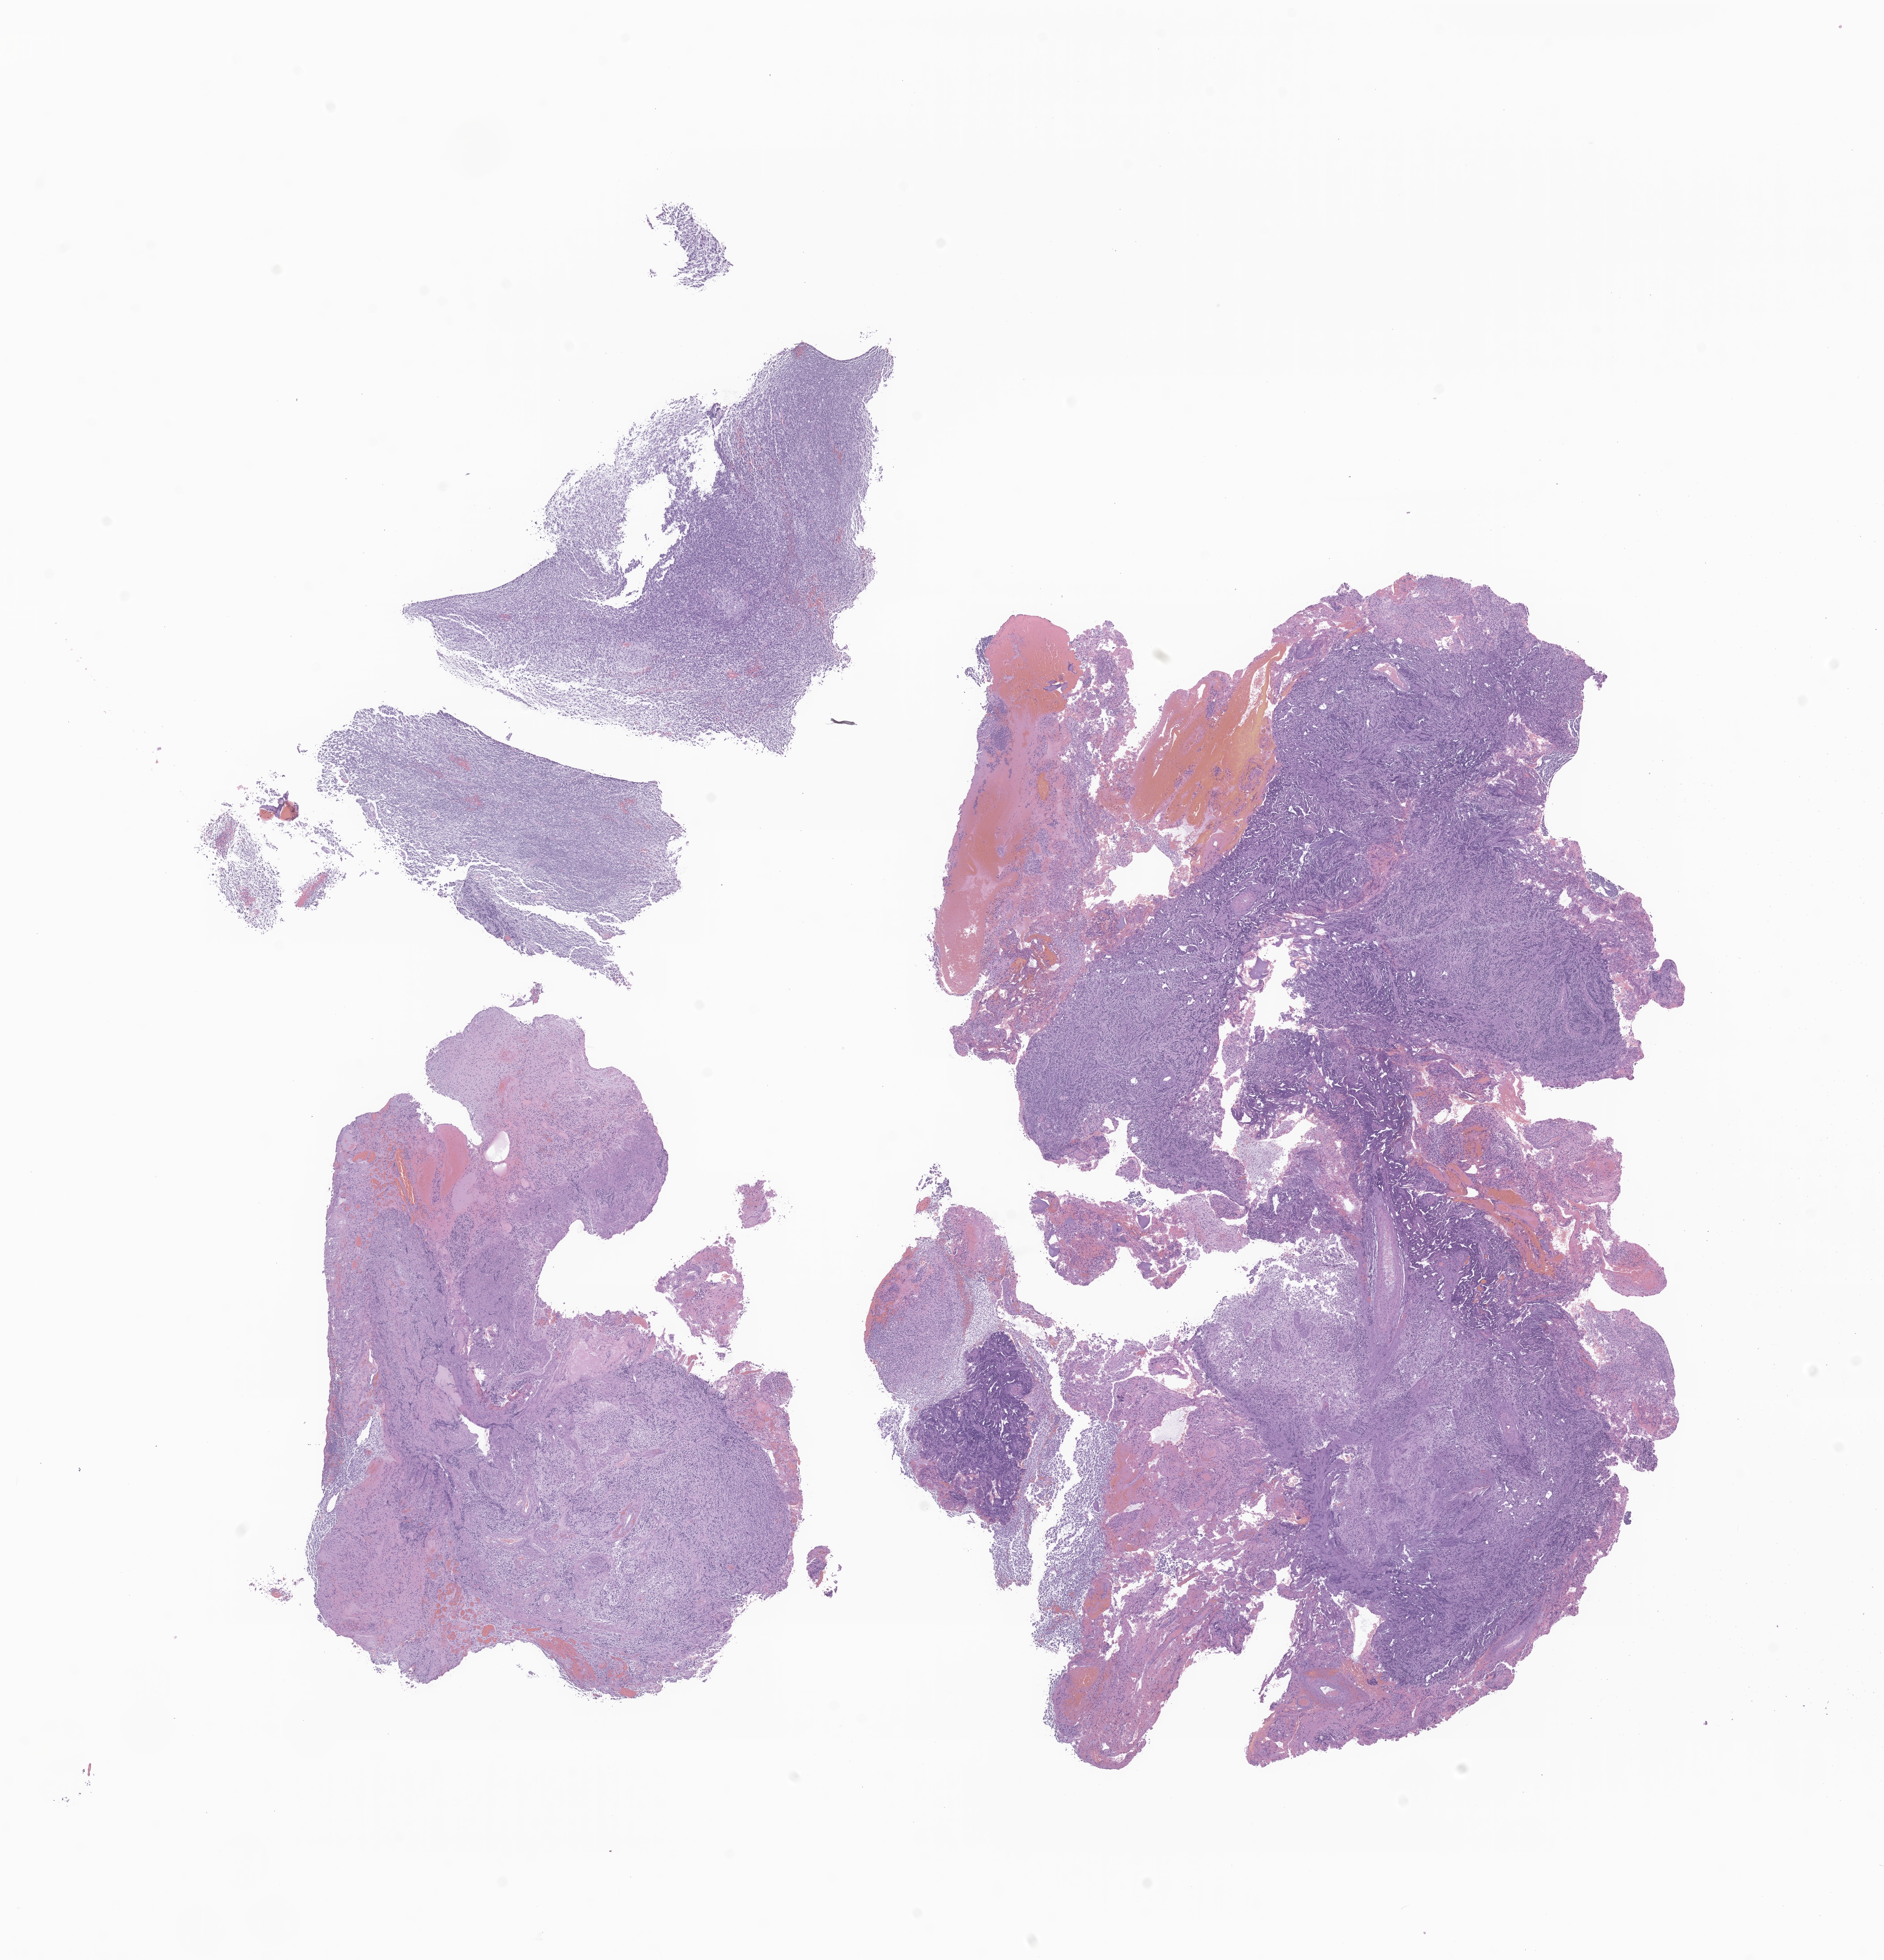
Hematoxylin and eosin (H&E) whole-slide image of tumor tissue from the brain, a low-resolution overview of the entire scanned area, about 17.7 x 18.4 mm. FFPE section. Patient: female, age 111 months.
• recorded diagnosis: Medulloblastoma, NOS